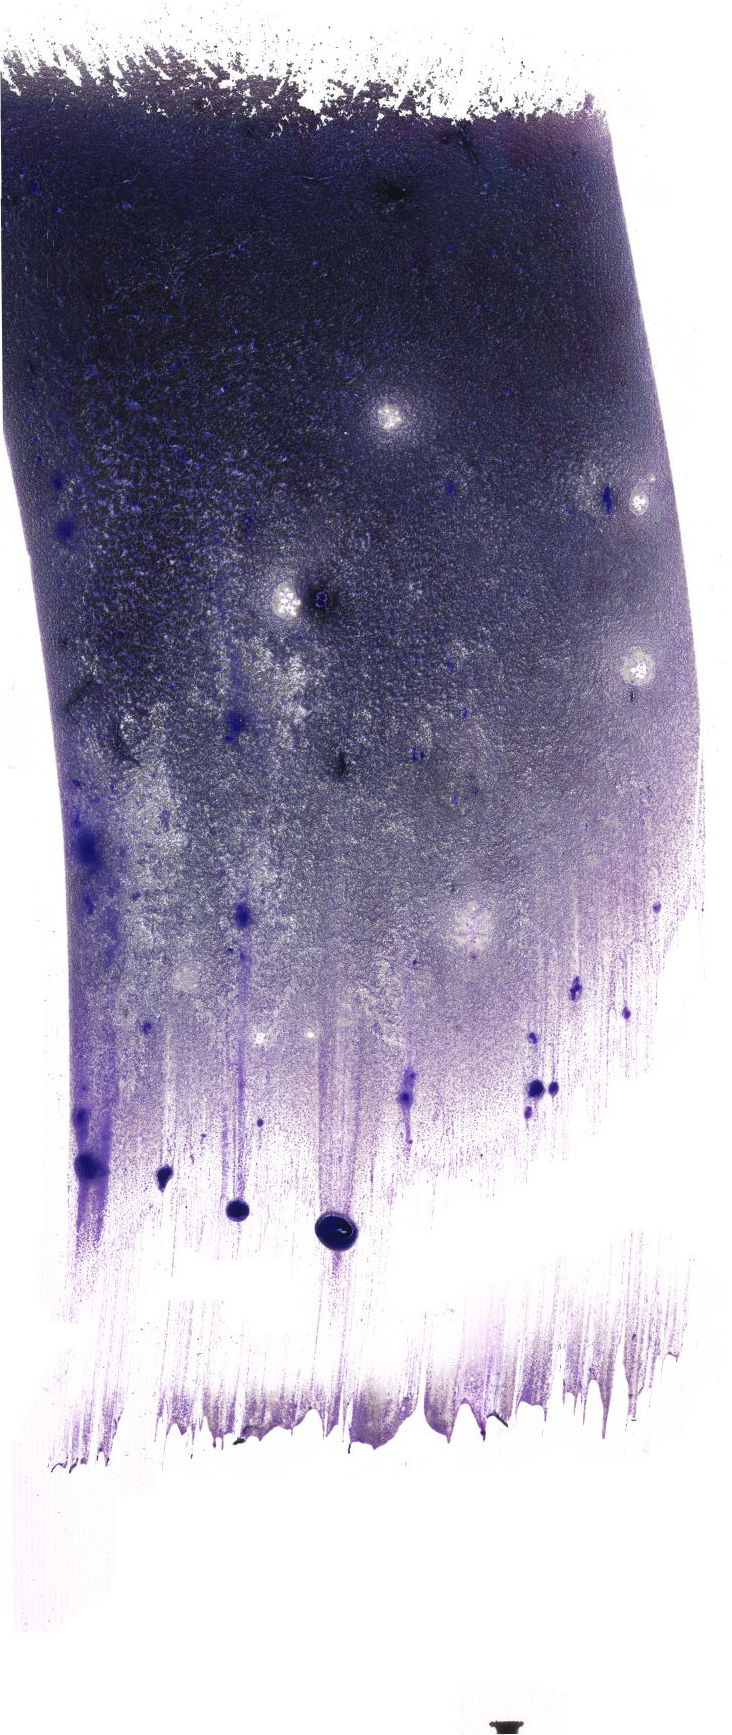
May-Grünwald–Giemsa-stained marrow aspirate smear (whole slide) — a low-resolution overview of the entire scanned area, about 20.7 x 49.2 mm. Patient sex: male.
Diagnosis: Chronic Phase Chronic Myeloid Leukemia, BCR-ABL1 Positive.